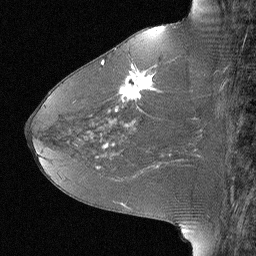
Breast MRI (dynamic contrast-enhanced), one sagittal slice; position 32 of 64 along the scan axis; dynamic contrast-enhanced study with each time point stored as its own series, time point 2 of 3 at this slice position (early post-contrast, ordered by acquisition time); 1.5 T; TE 4 ms, TR 30 ms; 2.25 mm slice thickness; 256 × 256 image matrix, field of view 180 × 180 mm. Female patient, age 46 years. Case-level facts recorded for this patient, not image findings: setting: breast cancer imaged before/during neoadjuvant chemotherapy; receptor status: HR-positive, HER2-negative.
Structures marked on this image (semi-automatically segmented with operator editing):
- analysis volume of interest (the breast-tissue region the enhancement analysis was run in; not a lesion): bounding box (x1, y1, x2, y2) in pixels: (106, 43, 184, 119)
- tumour enhancement mask (voxels above the 90 % enhancement threshold inside the analysis volume of interest): (109, 65, 159, 112)